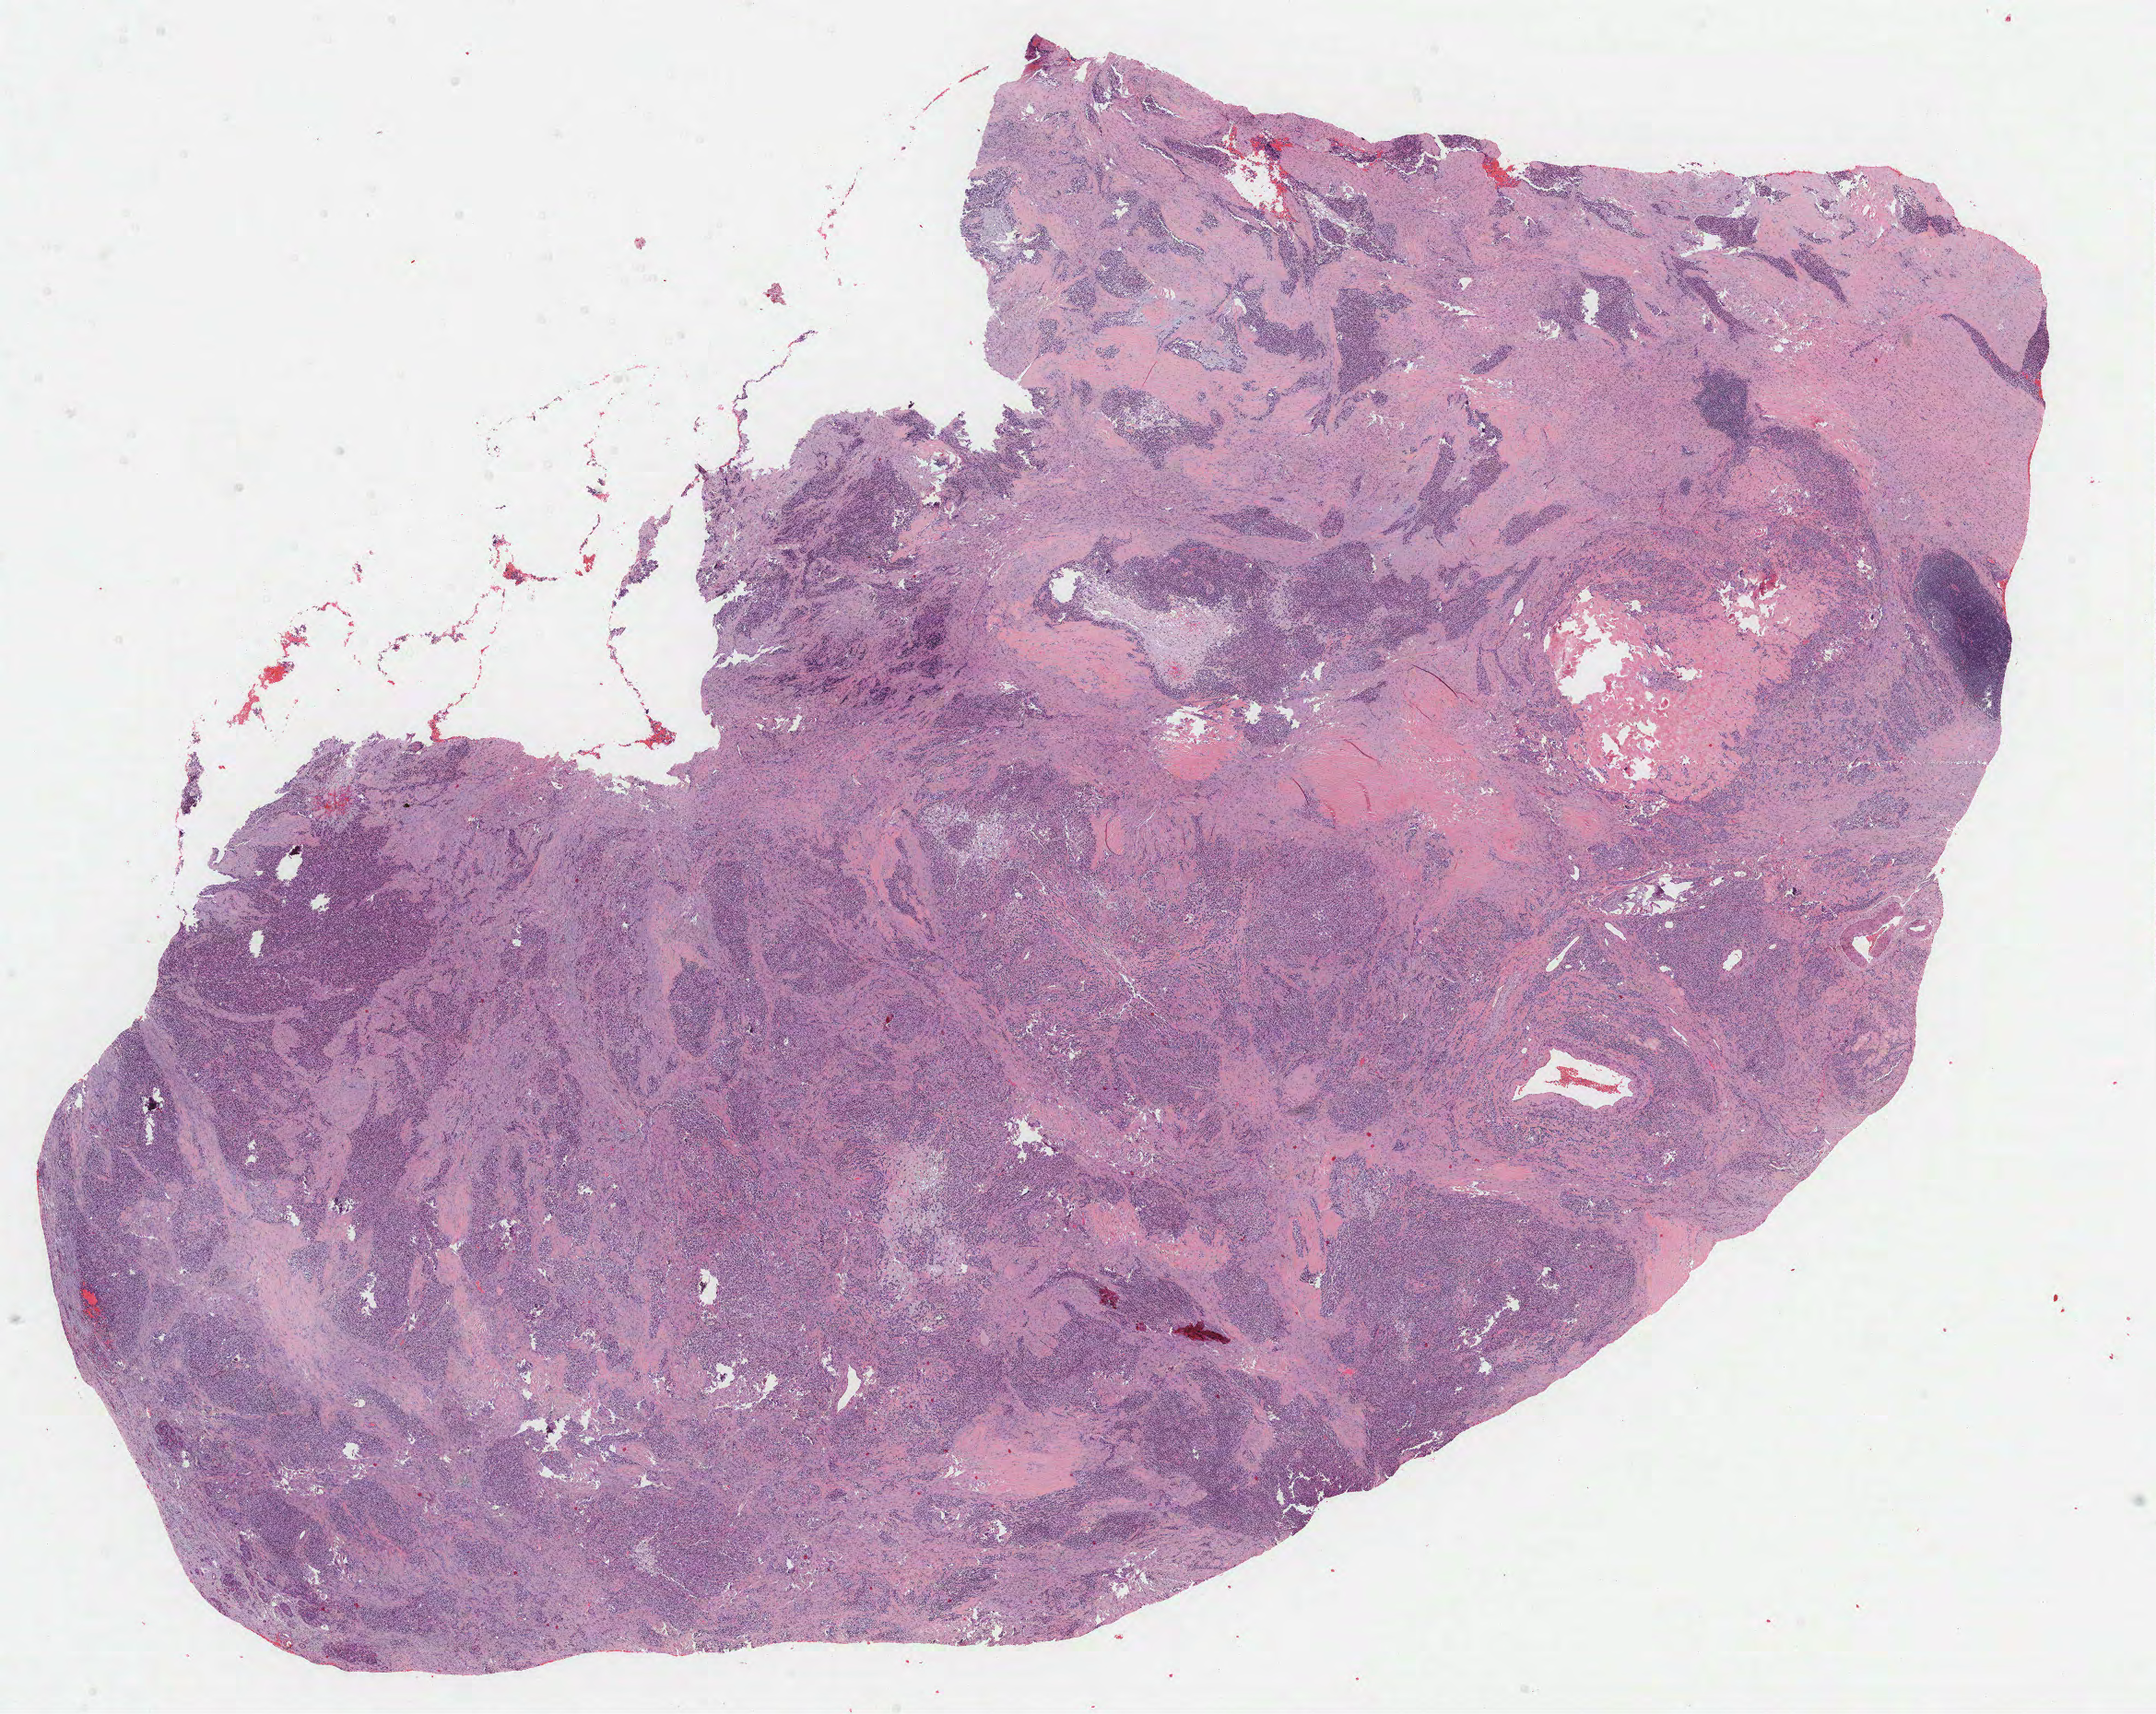
Whole-slide histology image, Hematoxylin and eosin (H&E) stained — shown as a low-resolution overview of the whole scanned area (about 18.9 x 15.0 mm, acquisition: 40x scan). Formalin-fixed paraffin-embedded (FFPE) diagnostic section. Primary tumour sample from the pancreas. Female patient; age at initial diagnosis 59 years. Histologic grade: G1 (well differentiated).
AJCC pathologic stage: IB (7th edition). Diagnosis: Neuroendocrine carcinoma, NOS. Lymph nodes positive (case pathology): 0 of 16 examined. TNM: T2 N0 MX.